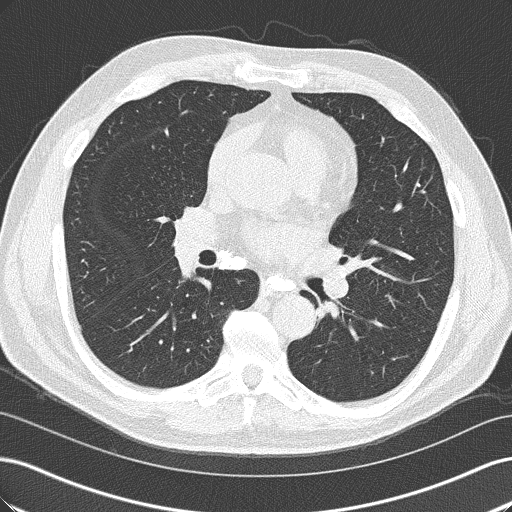
Chest CT (low-dose screening protocol), one axial image; first (baseline) screen; lung window (W 1500 / L -600 HU). Male, age 57 years at enrolment. Former smoker at enrolment.
Lesion marked by an expert reader, box from (x=300, y=285) to (x=360, y=342) px. Screening reader's record for this exam: no non-calcified nodule ≥4 mm recorded. Participant outcome: lung cancer diagnosed 363 days after this screen — squamous cell carcinoma, NOS, left lower lobe, moderately differentiated (G2), stage IIIB (AJCC 6th edition), 38 mm at pathology.